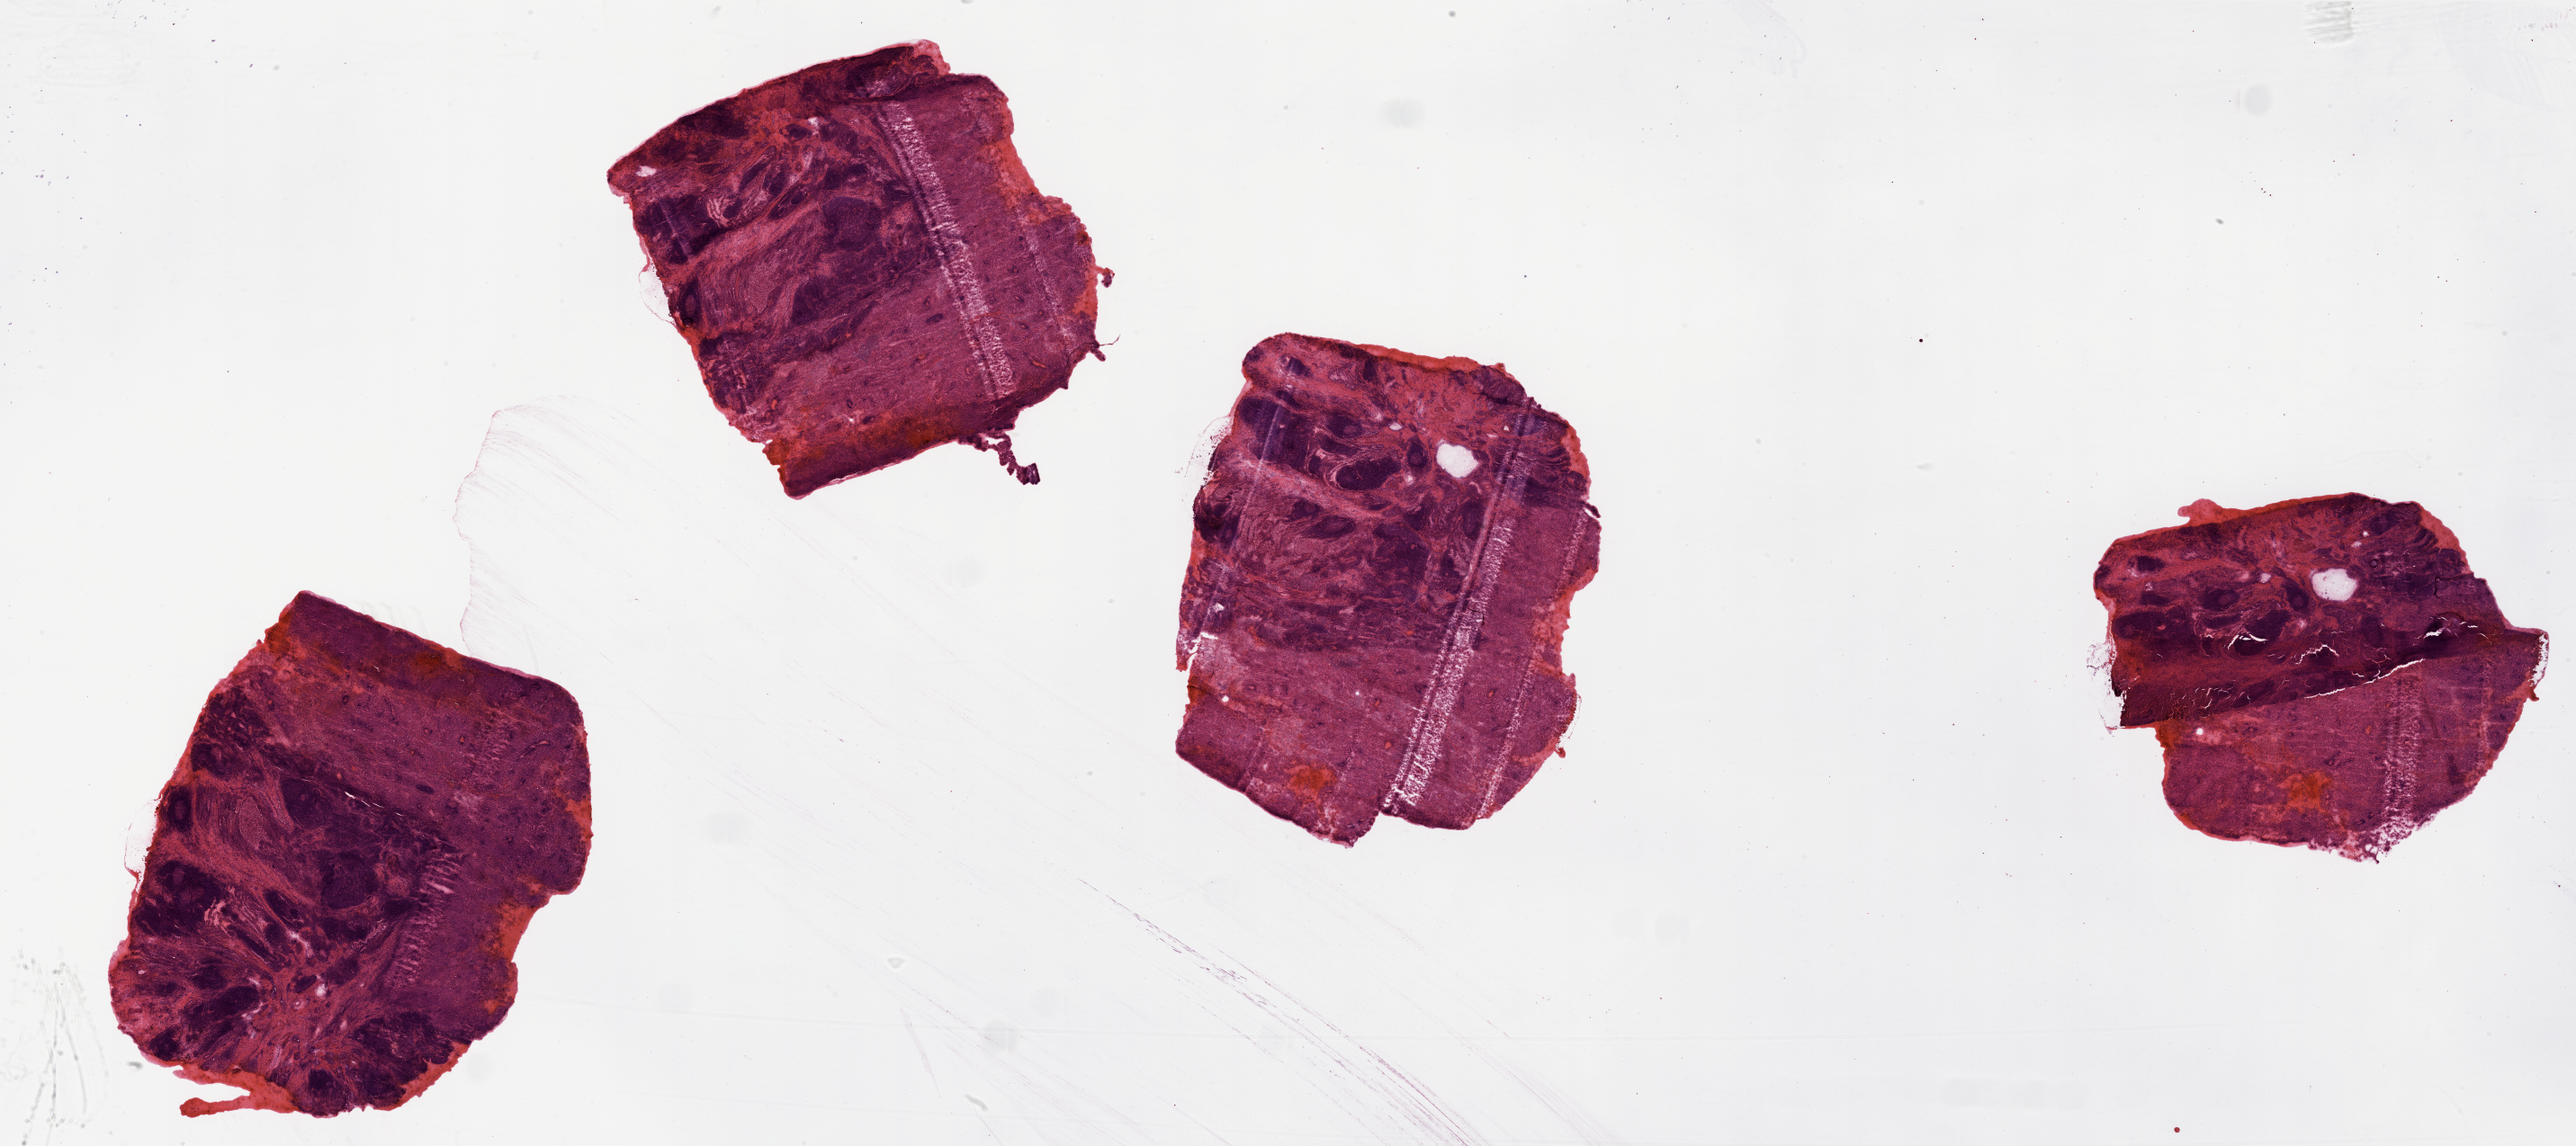
Digitized H&E-stained tissue section (whole slide) — low-resolution overview of the scanned area, about 45.3 x 20.2 mm (acquisition: 20x scan), lung, tumour tissue. 57-year-old male patient. Histologic grade: GX (grade cannot be assessed).
Primary tumour site (as recorded): right lower lobe. Diagnosis: Adenocarcinoma, NOS. AJCC pathologic stage: IIB.